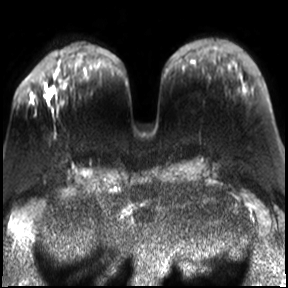
Breast MRI, one axial slice. Position 9 of 30 along the scan axis. Diffusion-weighted series; image 2 of 4 stored at this slice position (different b-values; order by instance number). 3 T. 4 mm slice thickness. 288 × 288 image matrix, field of view 340 × 340 mm. Female patient.
Annotated regions visible in this slice (manually delineated by an expert):
- tumour on diffusion-weighted imaging: bounding box <47,88,56,95> (left, top, right, bottom; pixels)